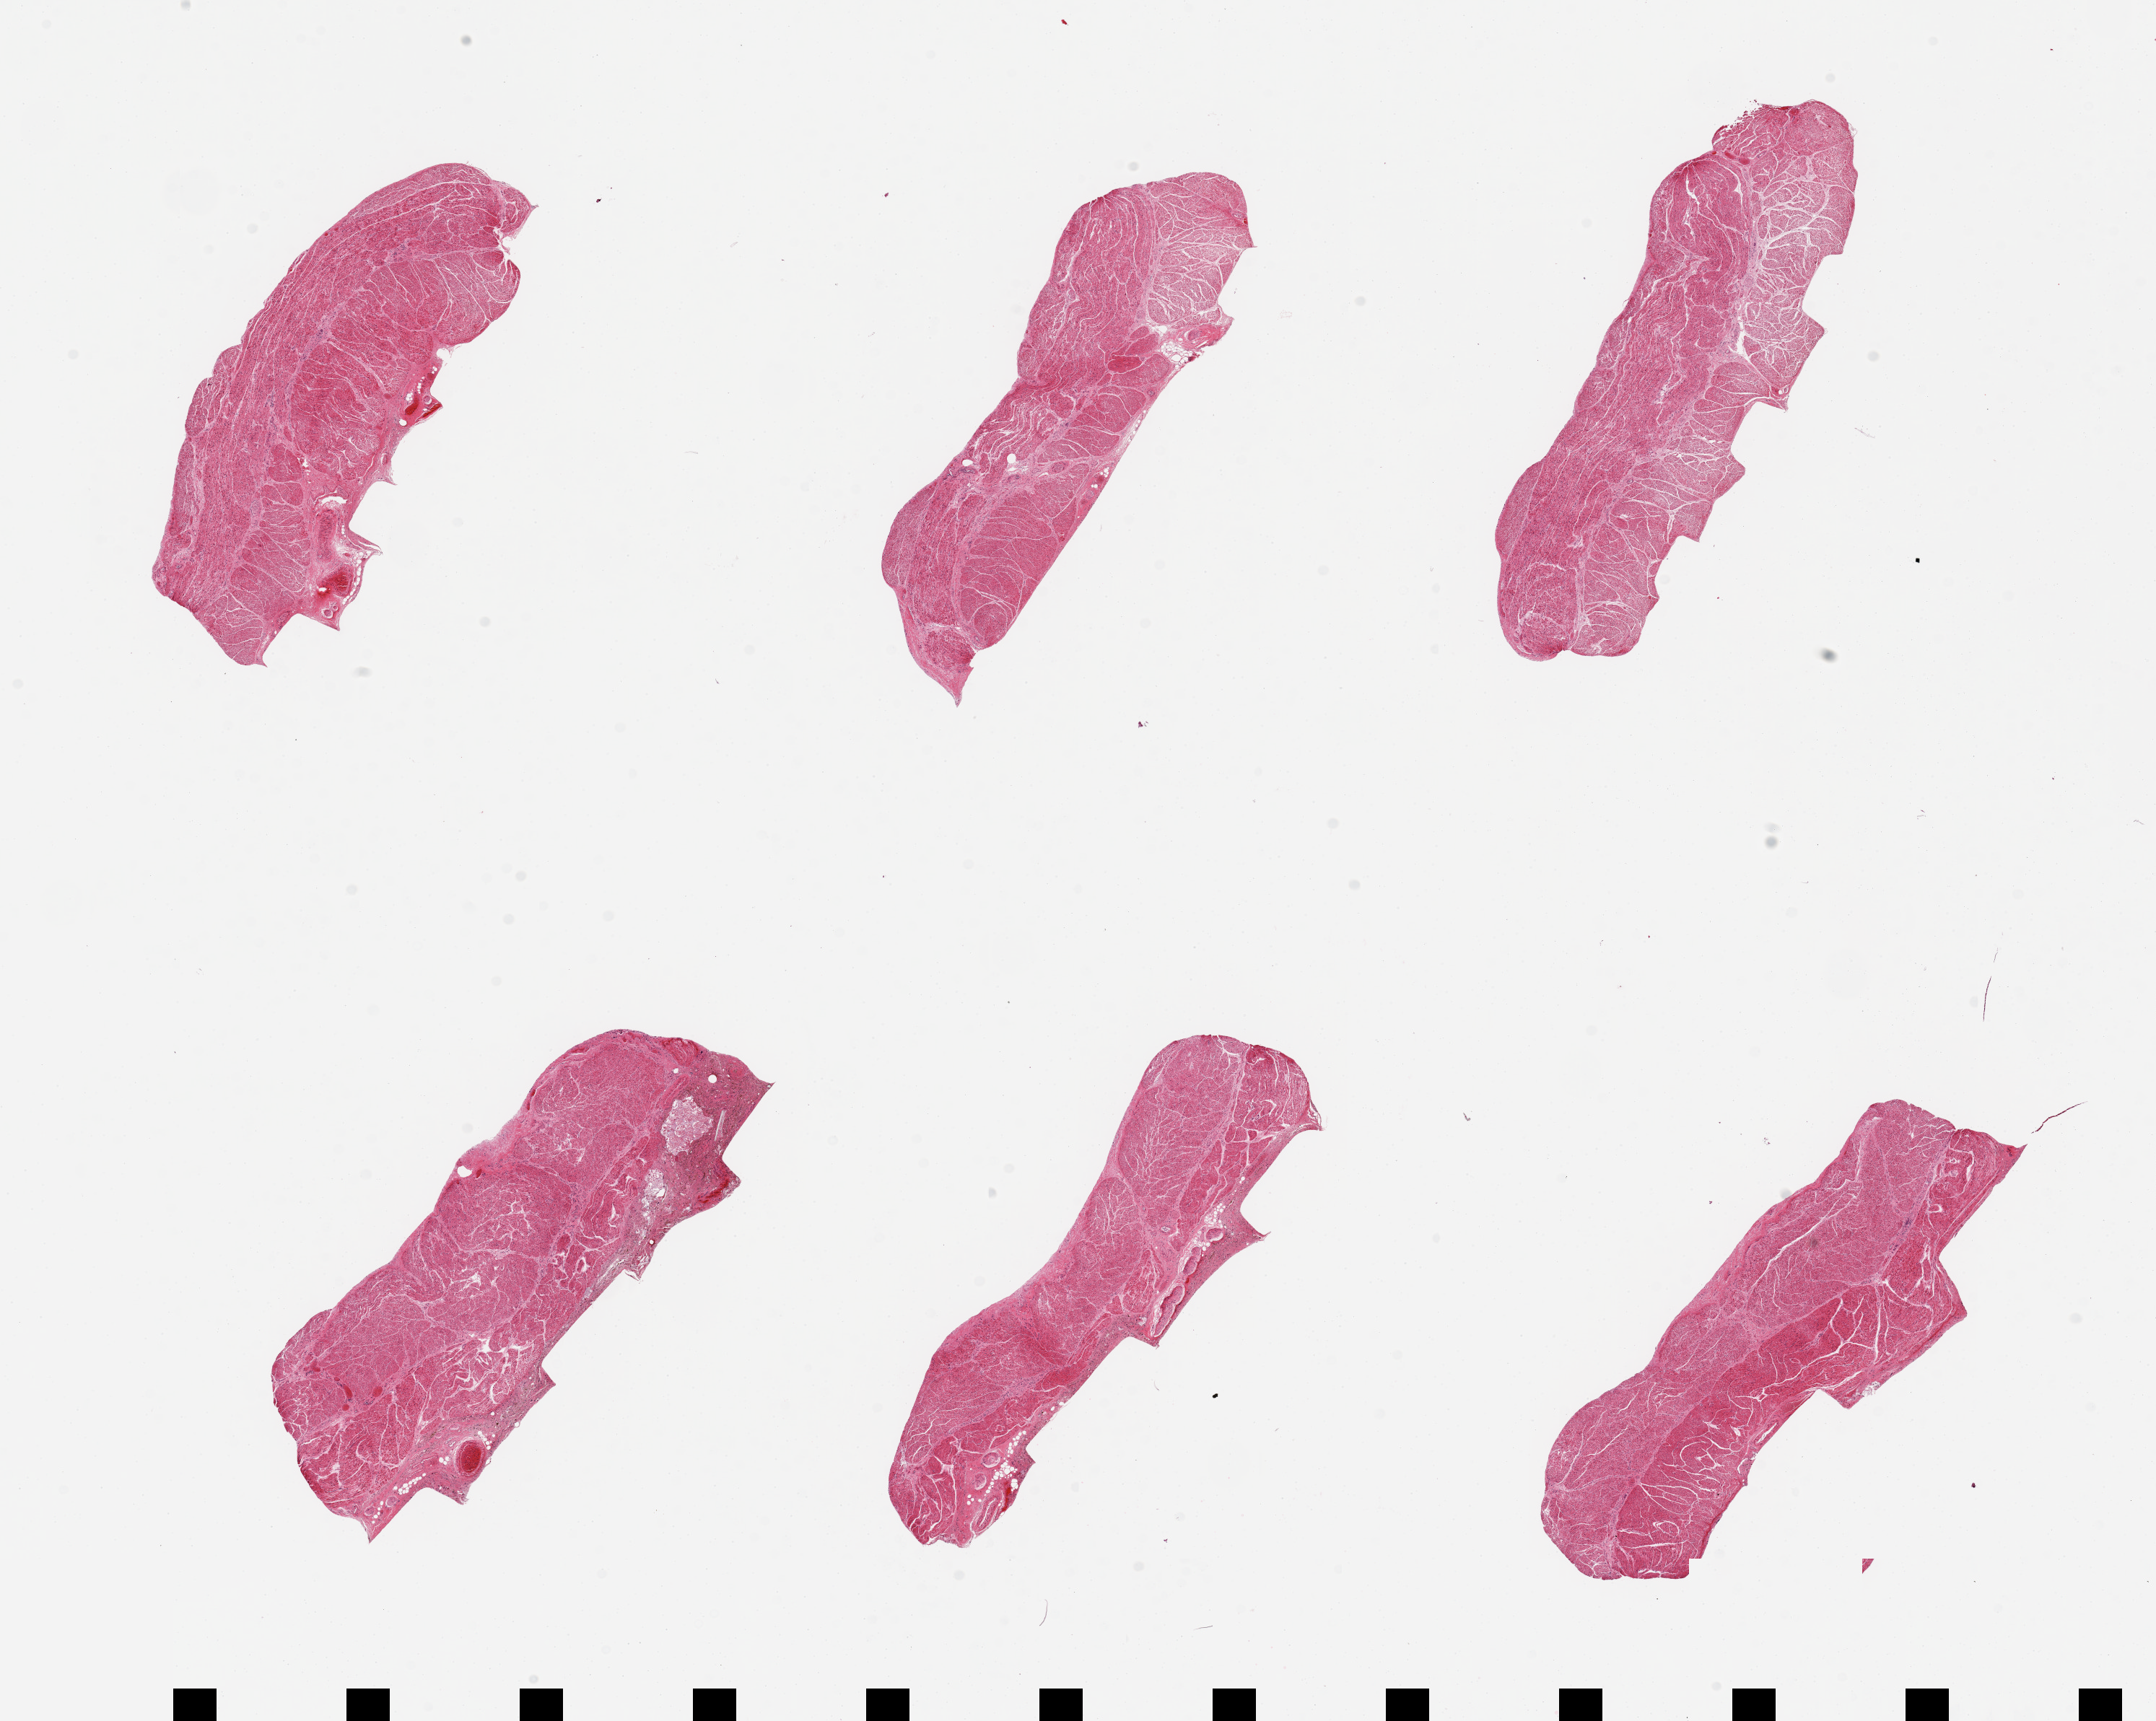
H&E whole-slide image, whole scanned area (about 23.6 x 18.9 mm, from a 20x scan) shown as a low-resolution overview. PAXgene-fixed, paraffin-embedded tissue. Section of esophageal muscle (target tissue). Tissue donor sample.
• reviewer comment on this tissue sample: 6 pieces; well dissected muscularis